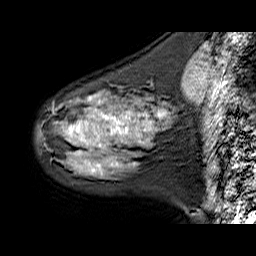
Breast MRI (dynamic contrast-enhanced), one sagittal slice; slice 19 of 60 in the series (ordered by position); dynamic contrast-enhanced series, time point 2 of 6 at this slice position (early post-contrast); 1.5 T; TE 6.3 ms, TR 32.9 ms; 256 × 256 image matrix, field of view 200 × 200 mm. Female patient. From the clinical record (not read from this slice): setting: breast cancer imaged before/during neoadjuvant chemotherapy; receptor status: HER2-positive.
Structures marked on this image (semi-automatically segmented with operator editing):
- analysis volume of interest (the breast-tissue region the enhancement analysis was run in; not a lesion): box from (x=38, y=81) to (x=174, y=178) px
- tumour enhancement mask (voxels above the 100 % enhancement threshold inside the analysis volume of interest): (x=69, y=99)–(x=165, y=172)